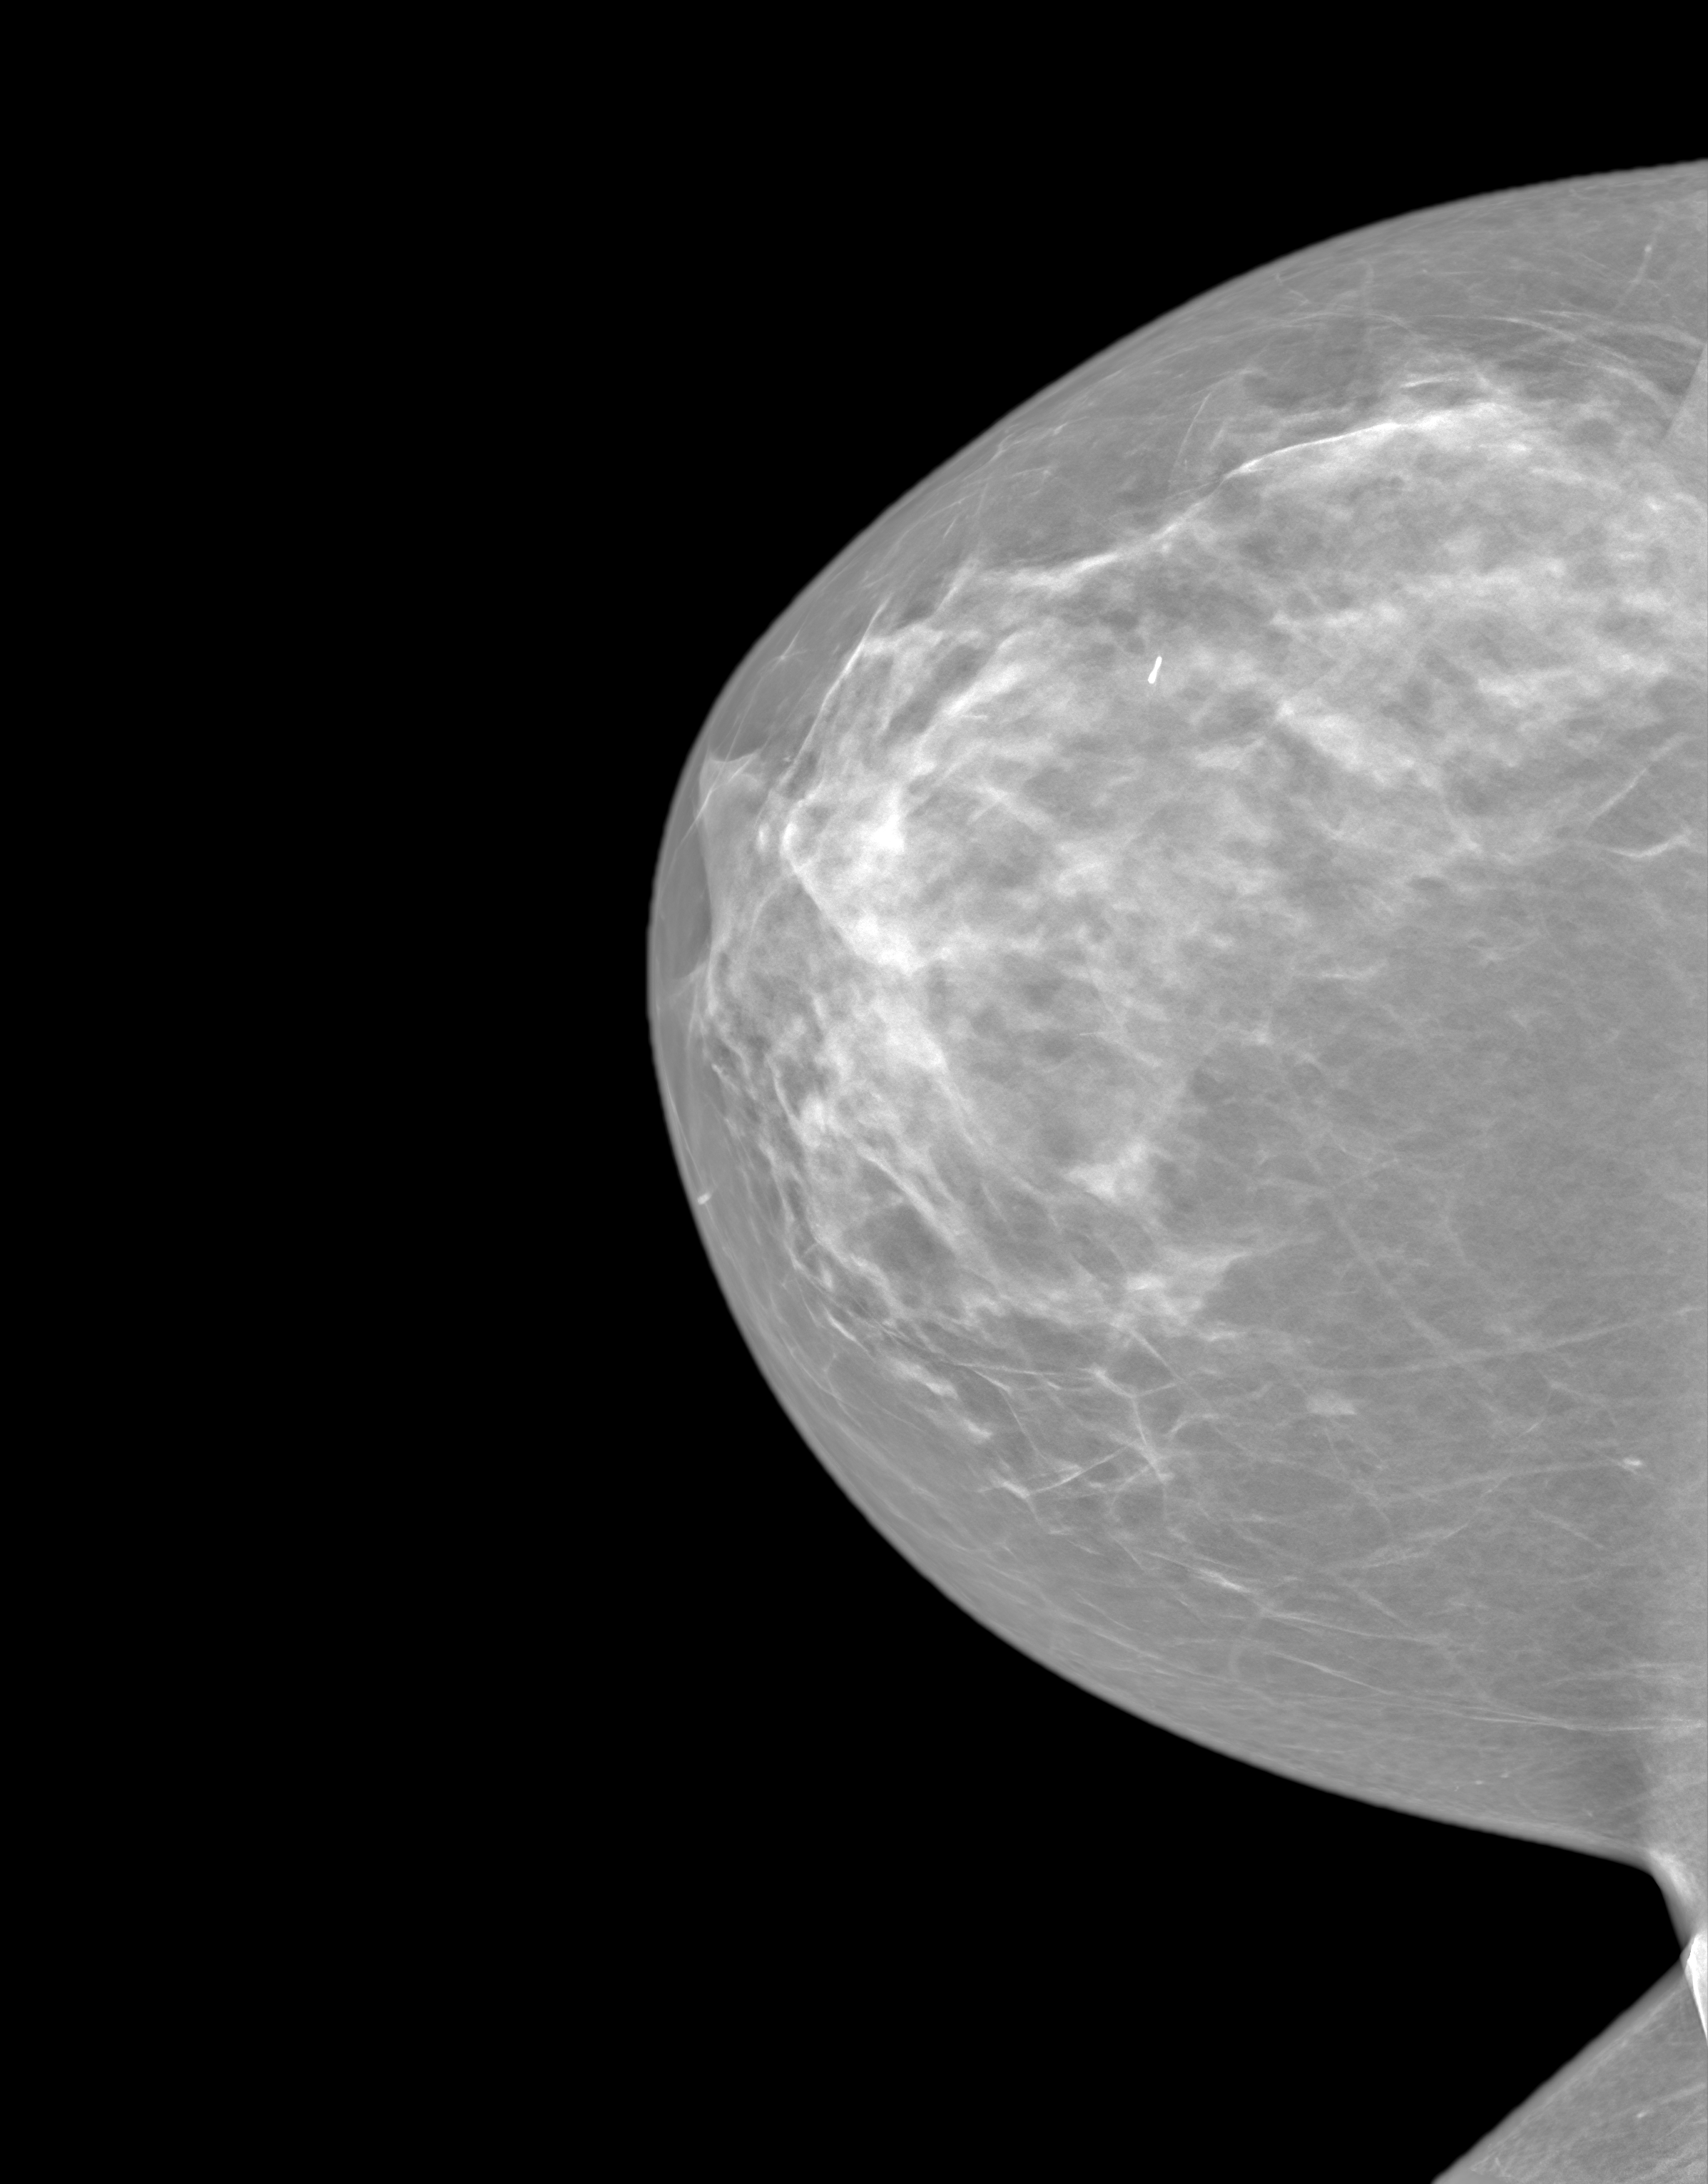
Screening examination. Female patient, age 43 years.
Image type: synthesized 2-D view from tomosynthesis. Breast: right. Projection: cranio-caudal projection.